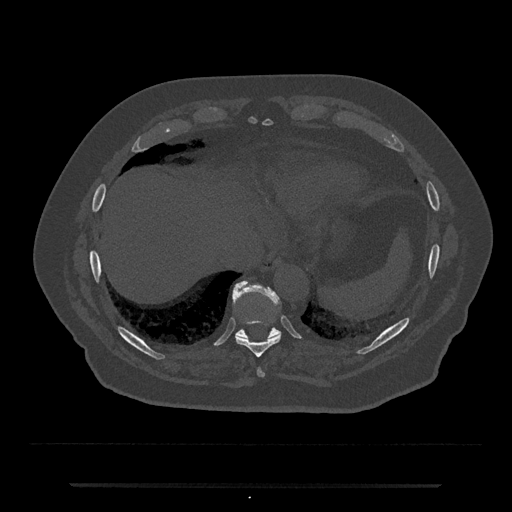
CT including the spine, one axial slice. Position 741 of 797 along the scan axis. Reconstruction kernel Br40s/3. 120 kVp. Bone window (W 1800 / L 400 HU). 0.5 mm slice thickness. 512 × 512 image matrix, field of view 434 × 434 mm. Patient: male, 80 years. From the clinical record (not read from this slice): primary cancer: prostate.
Outlined on this slice (semi-automatically segmented with operator editing):
- T10 vertebra: box from (x=233, y=282) to (x=280, y=338) px
- T8 vertebra: (x=257, y=369)–(x=264, y=377)
- T9 vertebra: (x=236, y=321)–(x=281, y=358)